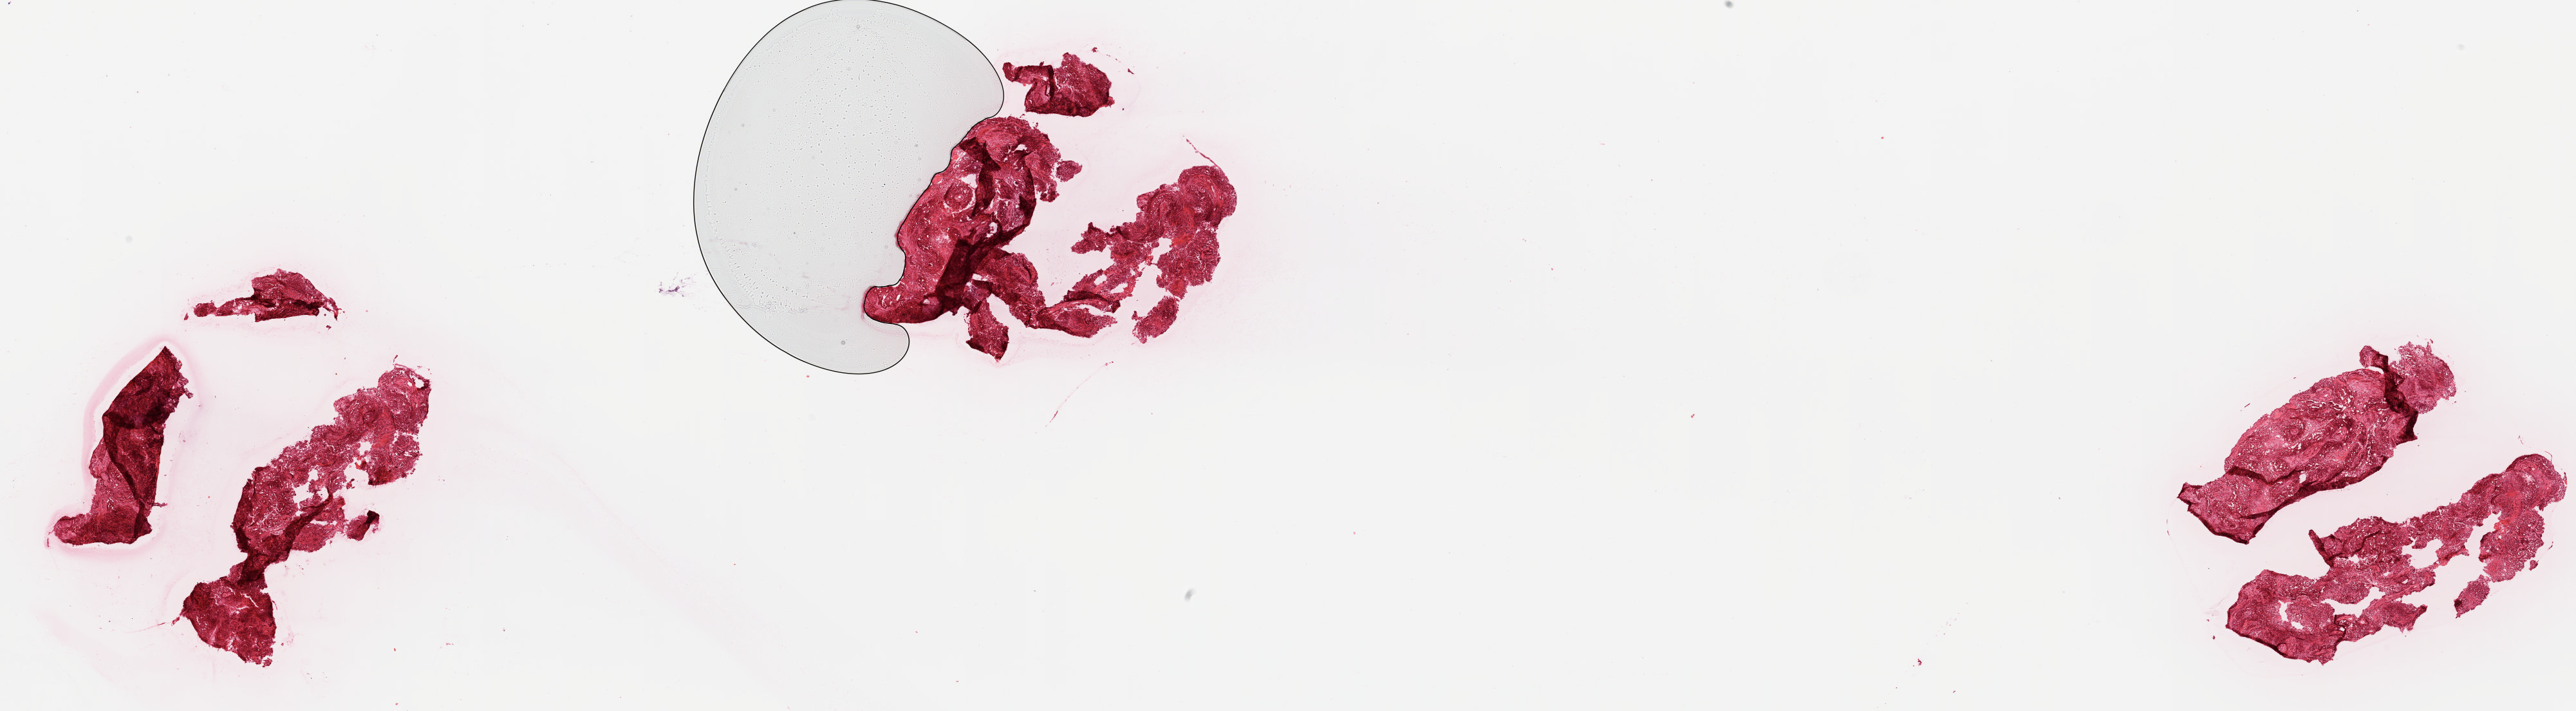
Digitized H&E tissue section (whole slide), shown as a low-resolution overview of the whole scanned area (about 31.7 x 8.8 mm, slide scanned at 20x); frozen section from the top of the tissue portion; sample: primary tumour, mesothelium. Male patient; age at initial diagnosis 68 years. Composition of this section per pathologist review: tumour cells 60%, tumour nuclei 60%, normal cells 0%, stromal cells 30%, necrosis 10%. Inflammatory infiltration, as recorded: lymphocyte infiltration 40%, monocyte infiltration 20%, neutrophil infiltration 20%.
TNM: T2 N0 M1. Diagnosis: Epithelioid mesothelioma, malignant (pleura, NOS). Laterality: right. AJCC pathologic stage: IV (7th edition).